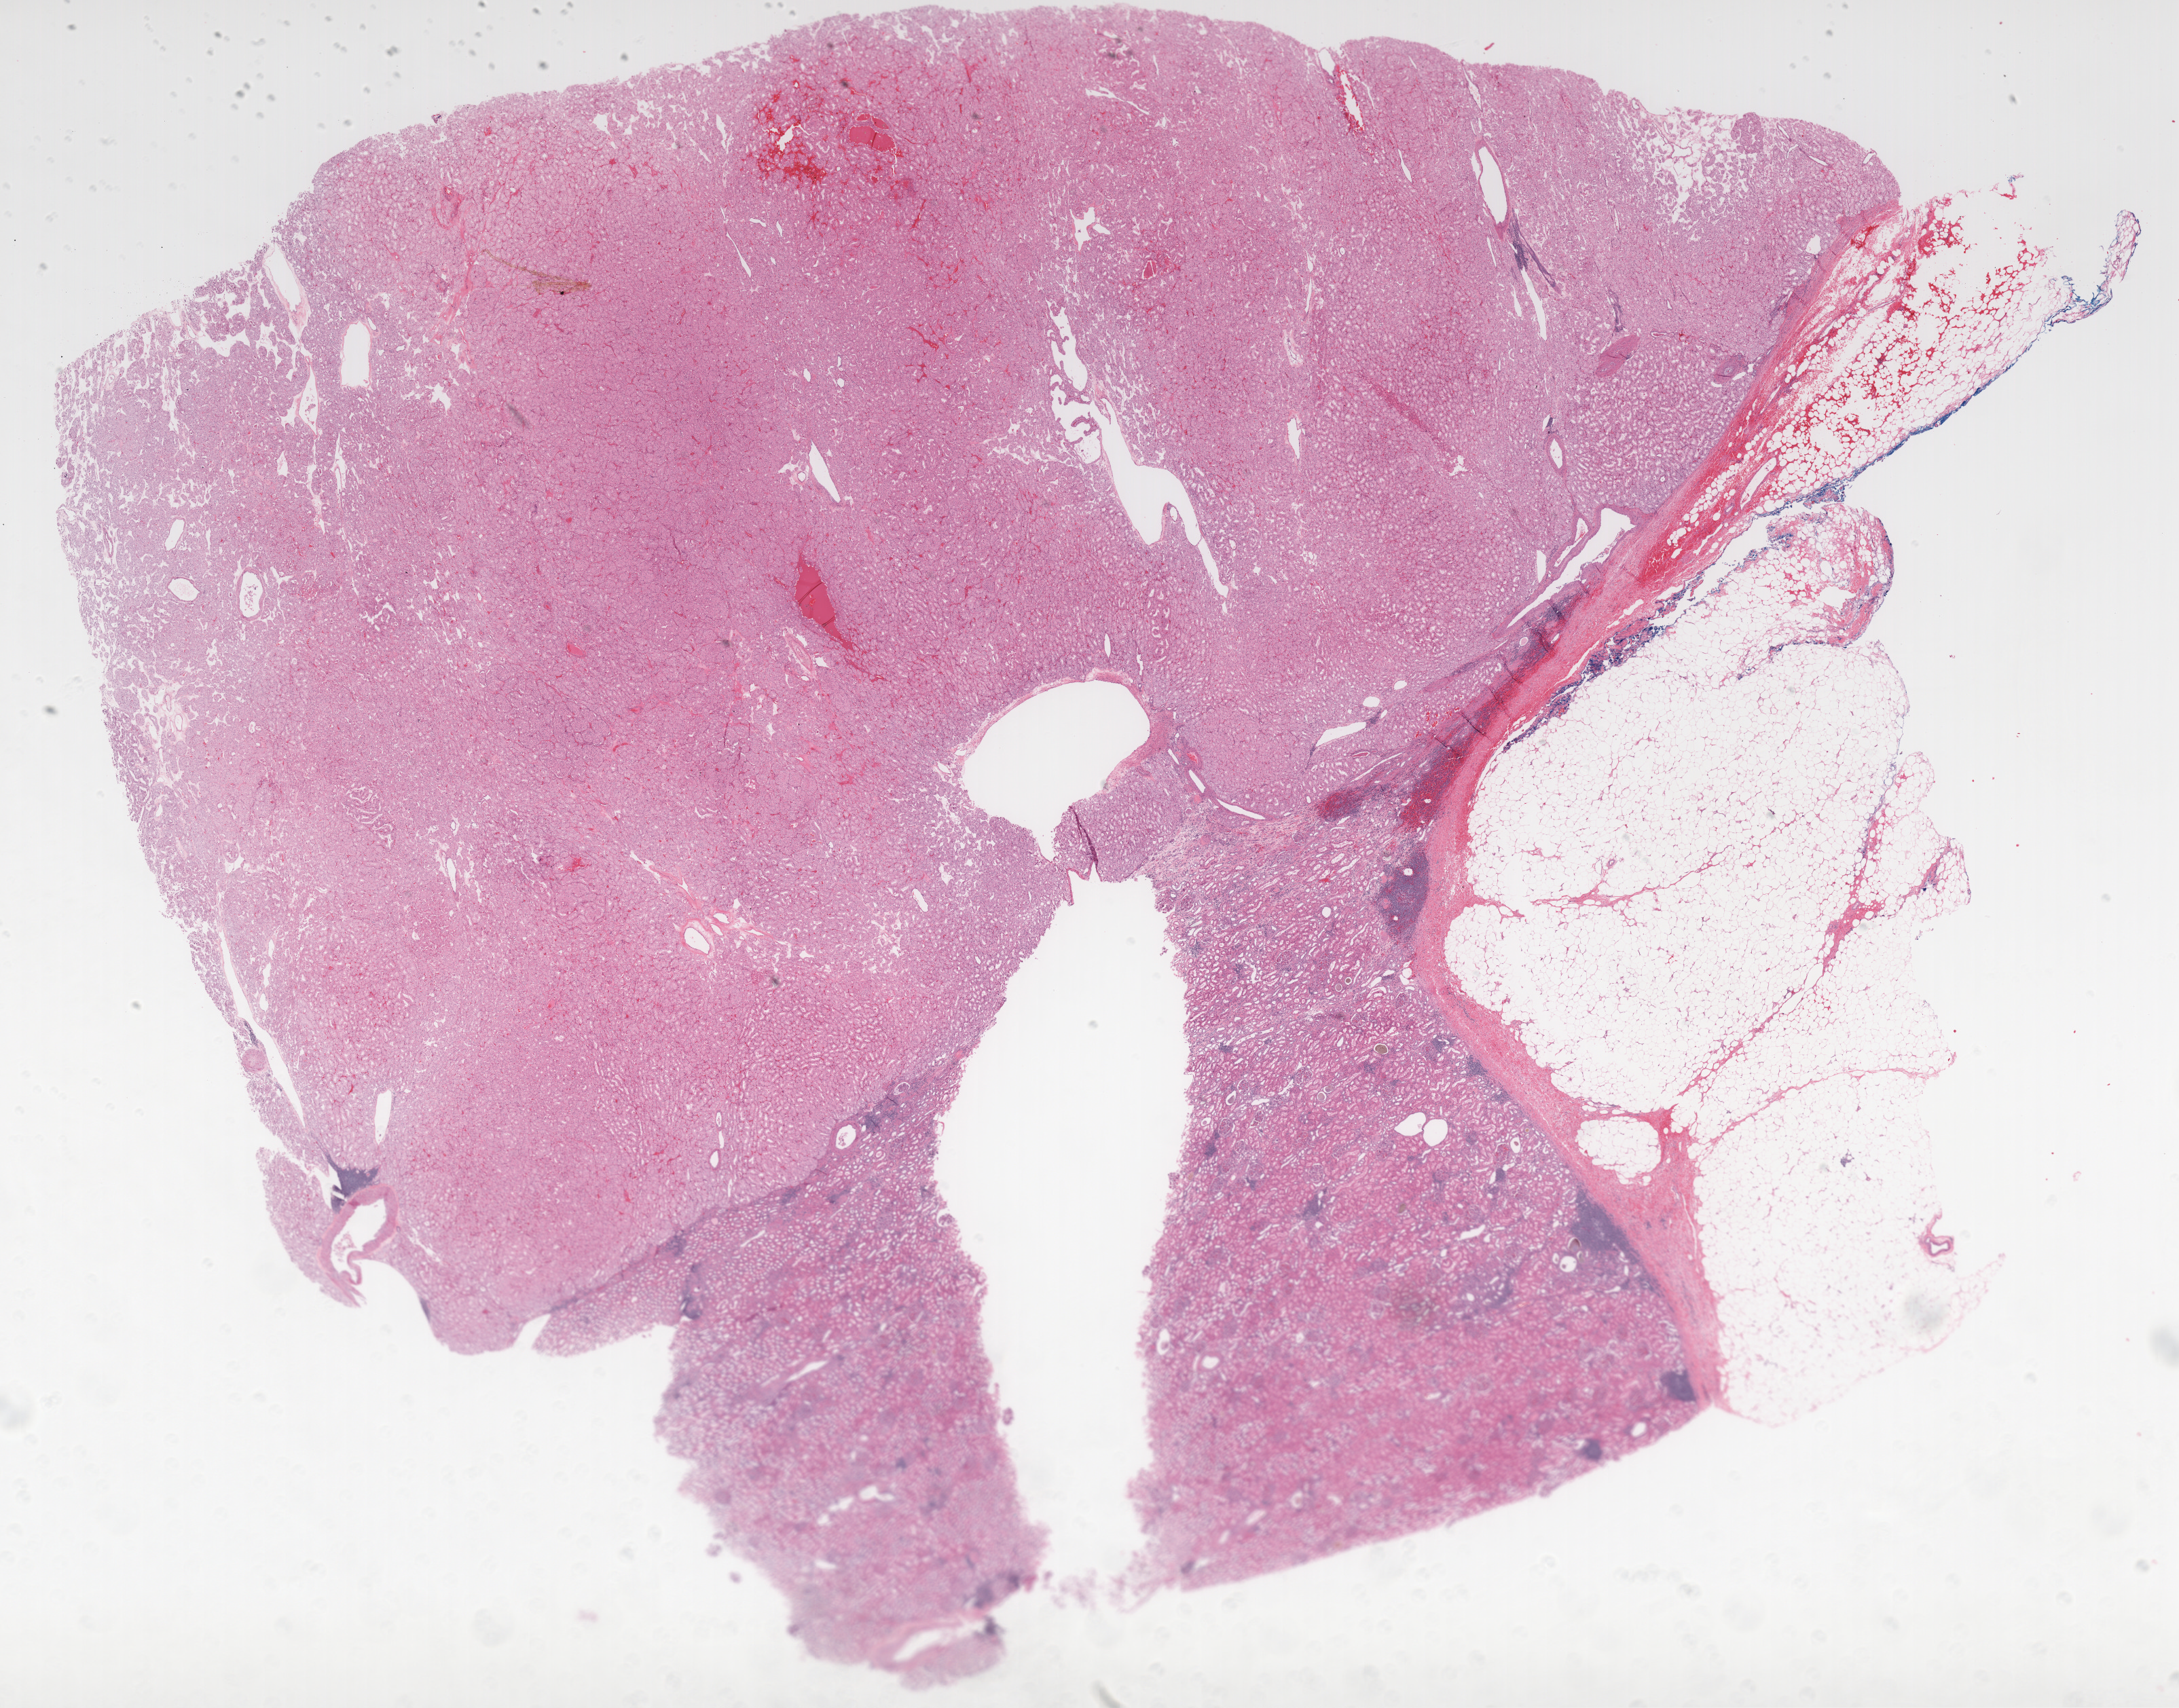
Hematoxylin and eosin (H&E) stained whole-slide image, a low-resolution overview of the entire scanned area, about 25.7 x 20.1 mm (acquisition: 40x scan). Formalin-fixed paraffin-embedded (FFPE) diagnostic section. Sample: primary tumour, kidney. Patient: male, age at initial diagnosis 69 years.
- AJCC pathologic stage: III
- TNM: T3a N0 M0
- diagnosis: Renal cell carcinoma, chromophobe type
- laterality: right